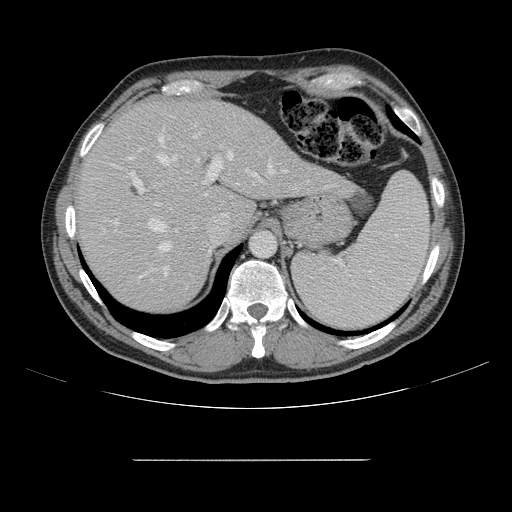
Contrast-enhanced abdominal CT, one axial slice. Position 115 of 164 along the scan axis. 120 kVp. Soft-tissue window (W 400 / L 40 HU). 2.5 mm slice thickness. 512 × 512 image matrix. Male patient, age 54 years. From the clinical record (not read from this slice): diagnosis: colorectal cancer liver metastases, imaged before liver resection; multiple liver metastases: yes; largest metastasis: 1 cm; disease in both lobes: no.
Outlined on this slice (expert manual segmentation):
- hepatic veins: bounding box <149,137,288,280> (left, top, right, bottom; pixels)
- liver: <77,101,342,310>
- planned liver remnant (the part of the liver to remain after resection): <77,101,247,311>
- portal vein (with intrahepatic branches): <115,128,258,291>